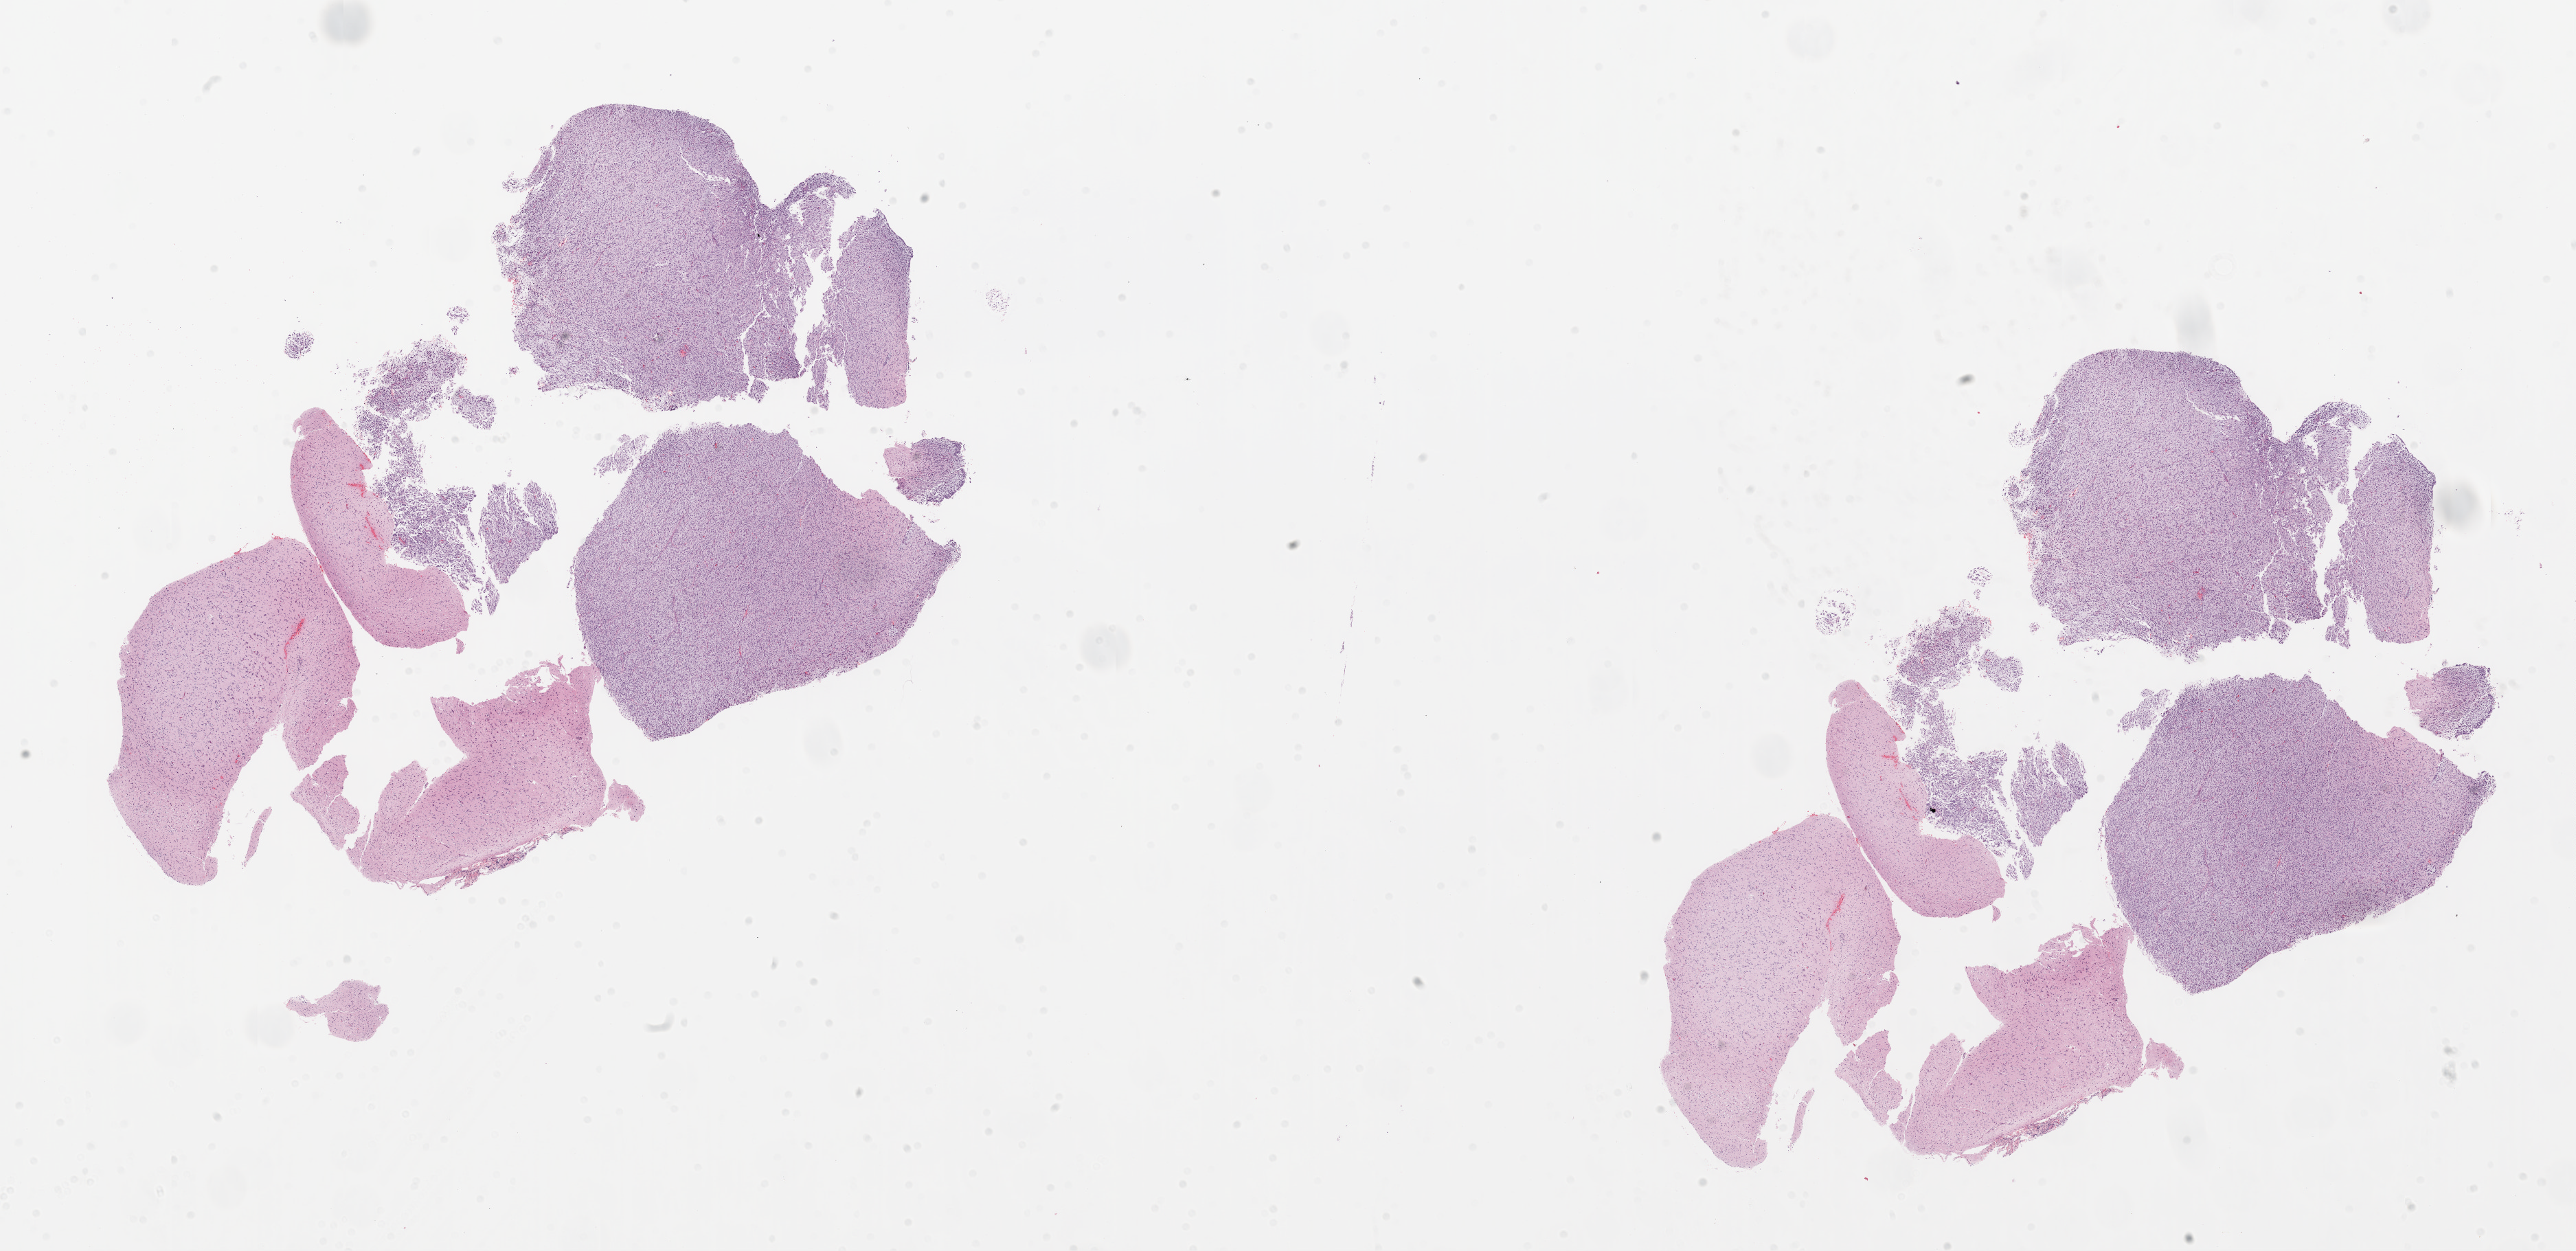
Digitized H&E-stained tissue section (whole slide) — a low-resolution overview of the entire scanned area, about 30.1 x 14.6 mm; formalin-fixed paraffin-embedded (FFPE) diagnostic section; brain, primary tumour sample. Female patient; age at initial diagnosis 17 years.
Diagnosis: Glioblastoma.